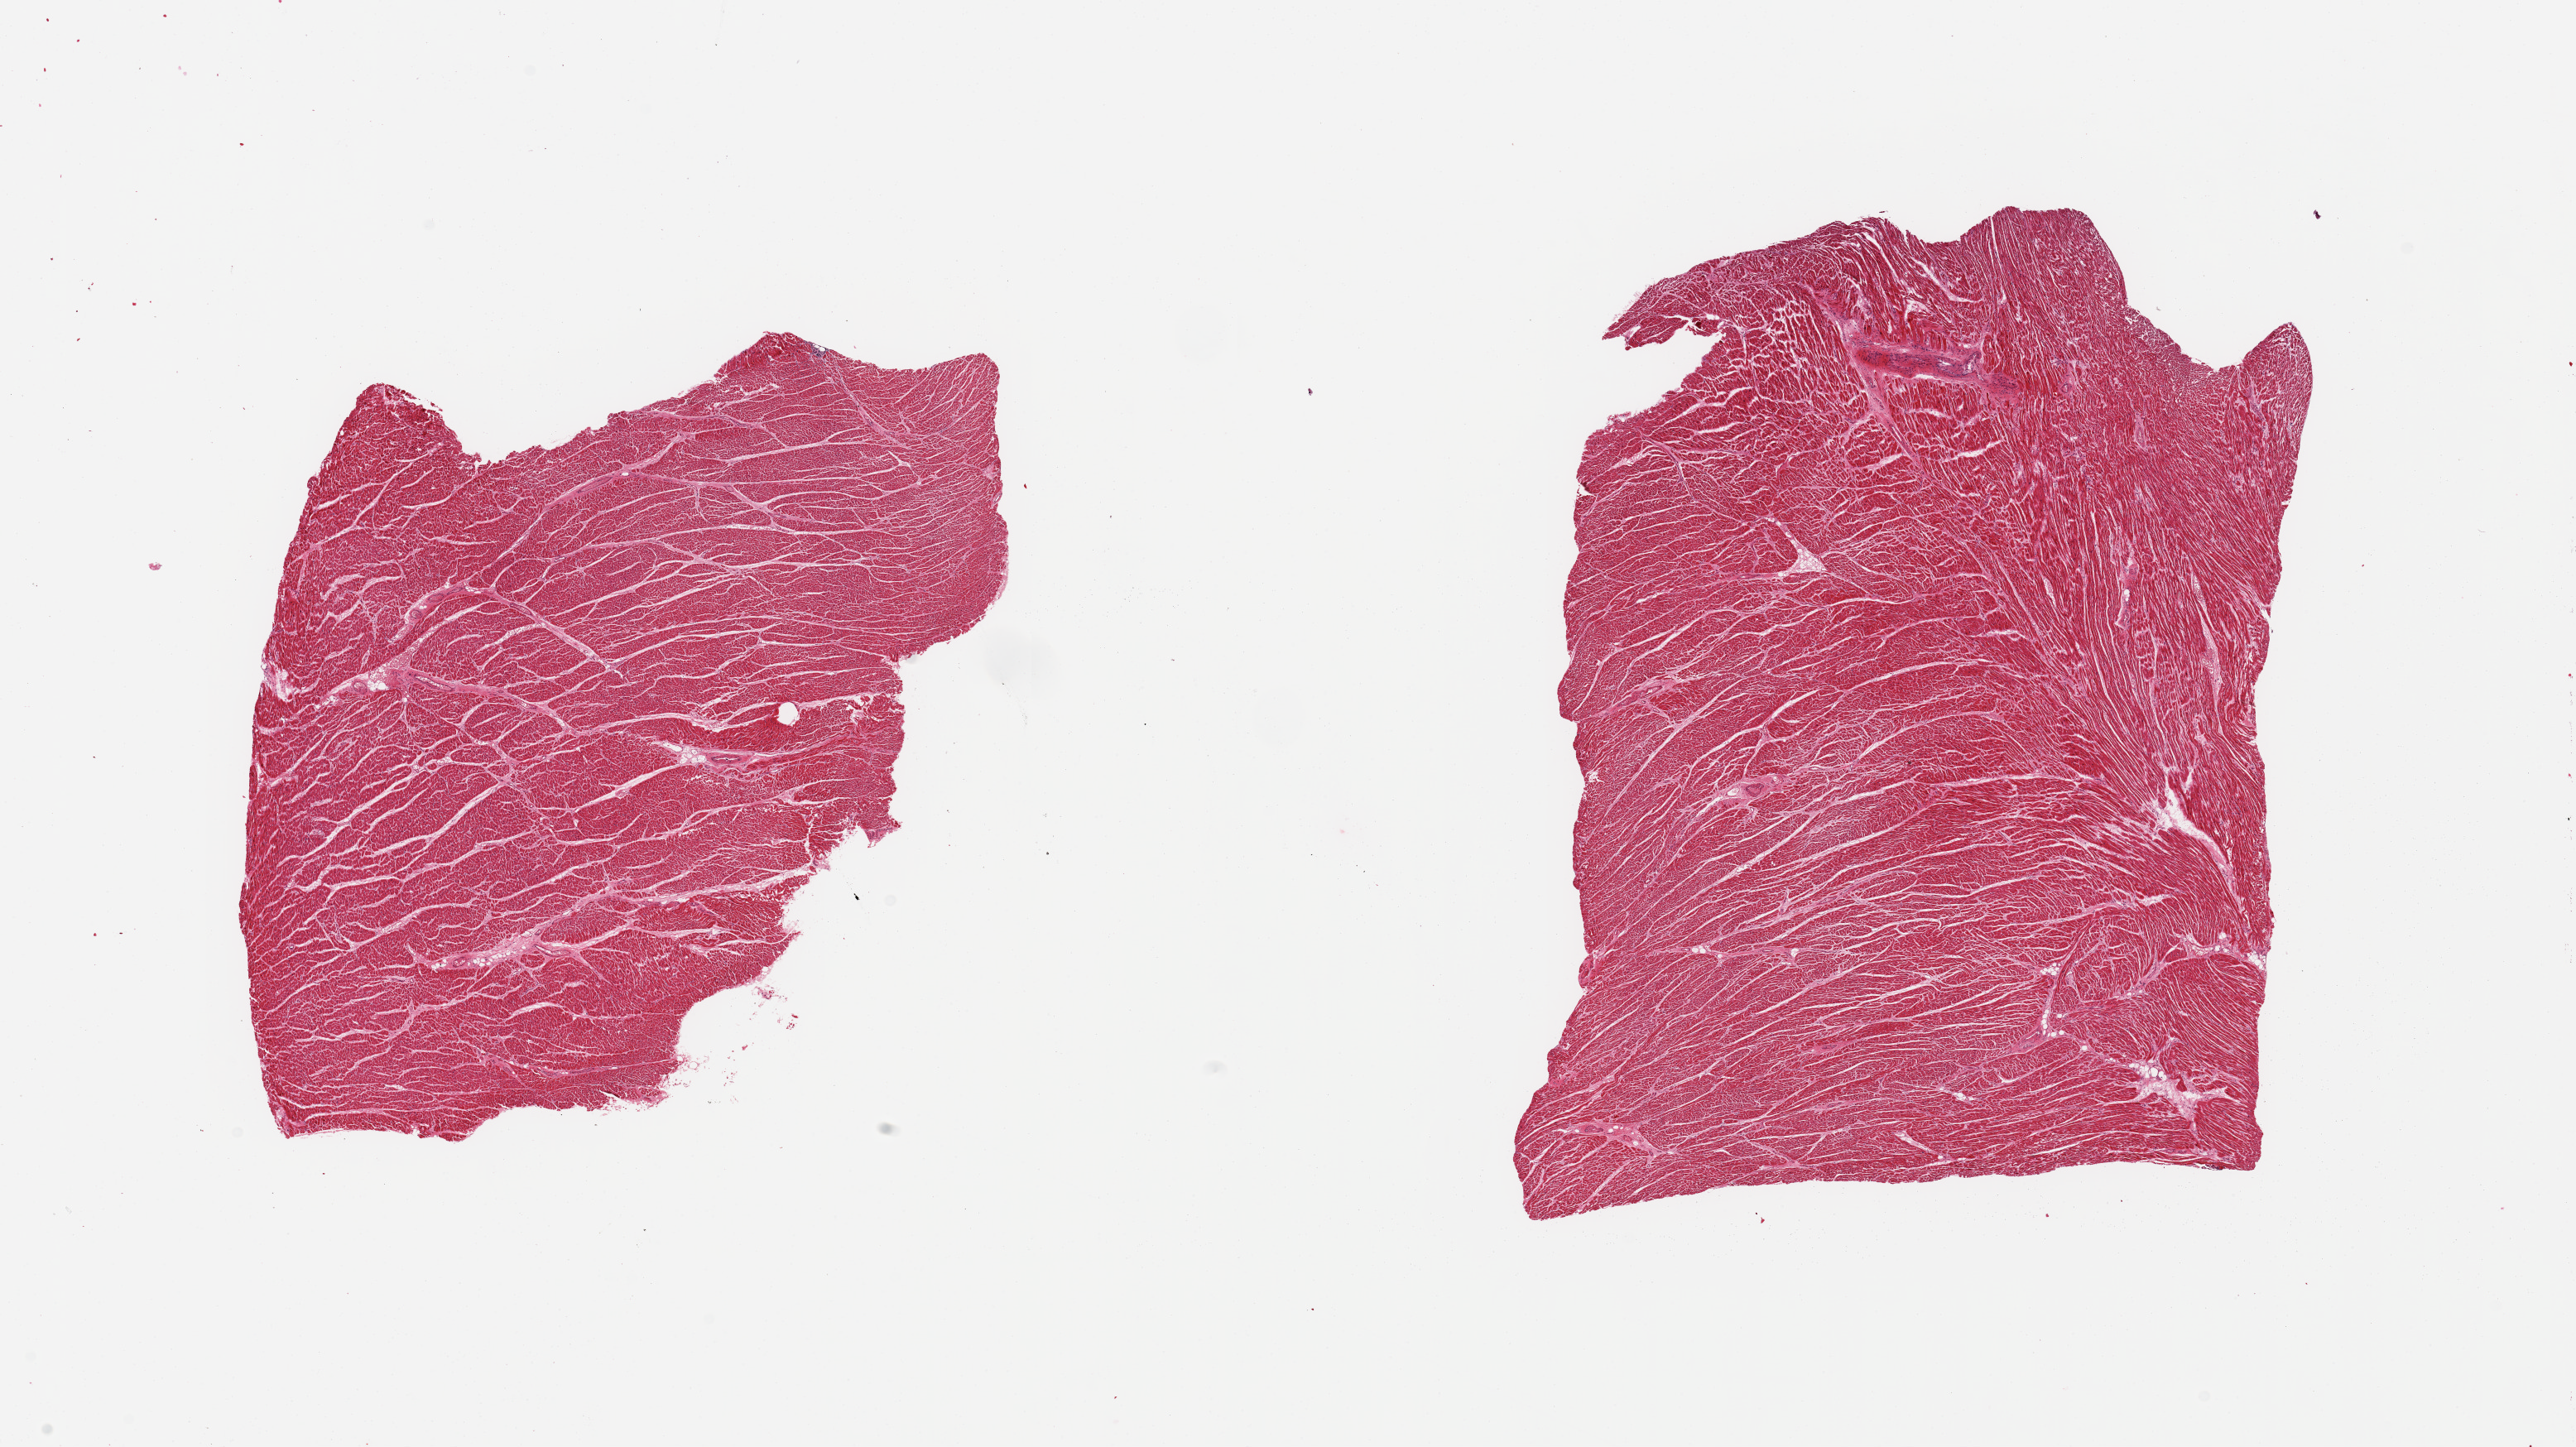
Haematoxylin and eosin whole-slide image — whole scanned area (about 24.6 x 13.8 mm, from a 20x scan) shown as a low-resolution overview. PAXgene-fixed, paraffin-embedded tissue. Sampled site (target tissue): heart. Donor tissue sample. Male donor.
• review note (as recorded): 2 pieces, minimal fibrosis